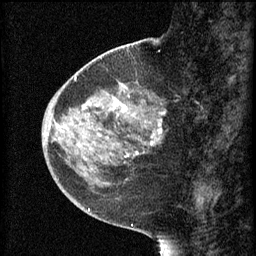
Breast MRI (dynamic contrast-enhanced), one sagittal slice; 3 images stored at this slice position (order not interpretable as contrast timing); 1.5 T; TE 4.2 ms, TR 8.2 ms; 2 mm slice thickness; 256 × 256 image matrix, field of view 180 × 180 mm. Female patient, age 44 years.
Structures marked on this image (semi-automatic segmentation, software-assisted and operator-edited):
- analysis volume of interest (the breast-tissue region the enhancement analysis was run in; not a lesion): bounding box (x1, y1, x2, y2) in pixels: (73, 82, 169, 165)
- tumour enhancement mask (voxels above the 70 % enhancement threshold inside the analysis volume of interest): (88, 96, 166, 157)